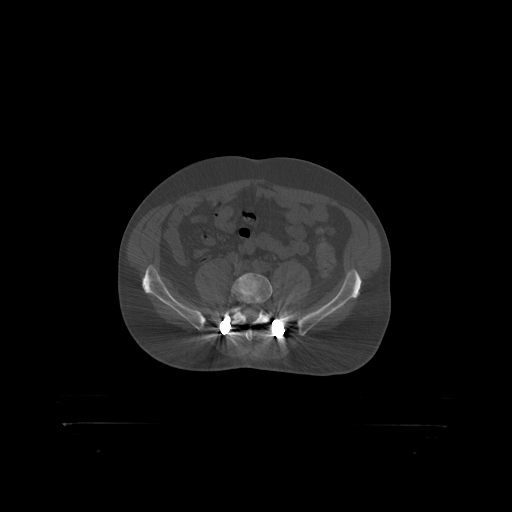
CT including the spine, one axial slice; position 199 of 399 along the scan axis; reconstruction kernel STANDARD; bone window (W 1800 / L 400 HU); 1.25 mm slice thickness; 512 × 512 image matrix, field of view 650 × 650 mm. Male patient, age 46 years. Case-level facts recorded for this patient, not image findings: primary cancer: skin.
Outlined on this slice (semi-automatically segmented with operator editing):
- L5 vertebra: bounding box (x1, y1, x2, y2) in pixels: (232, 273, 273, 319)